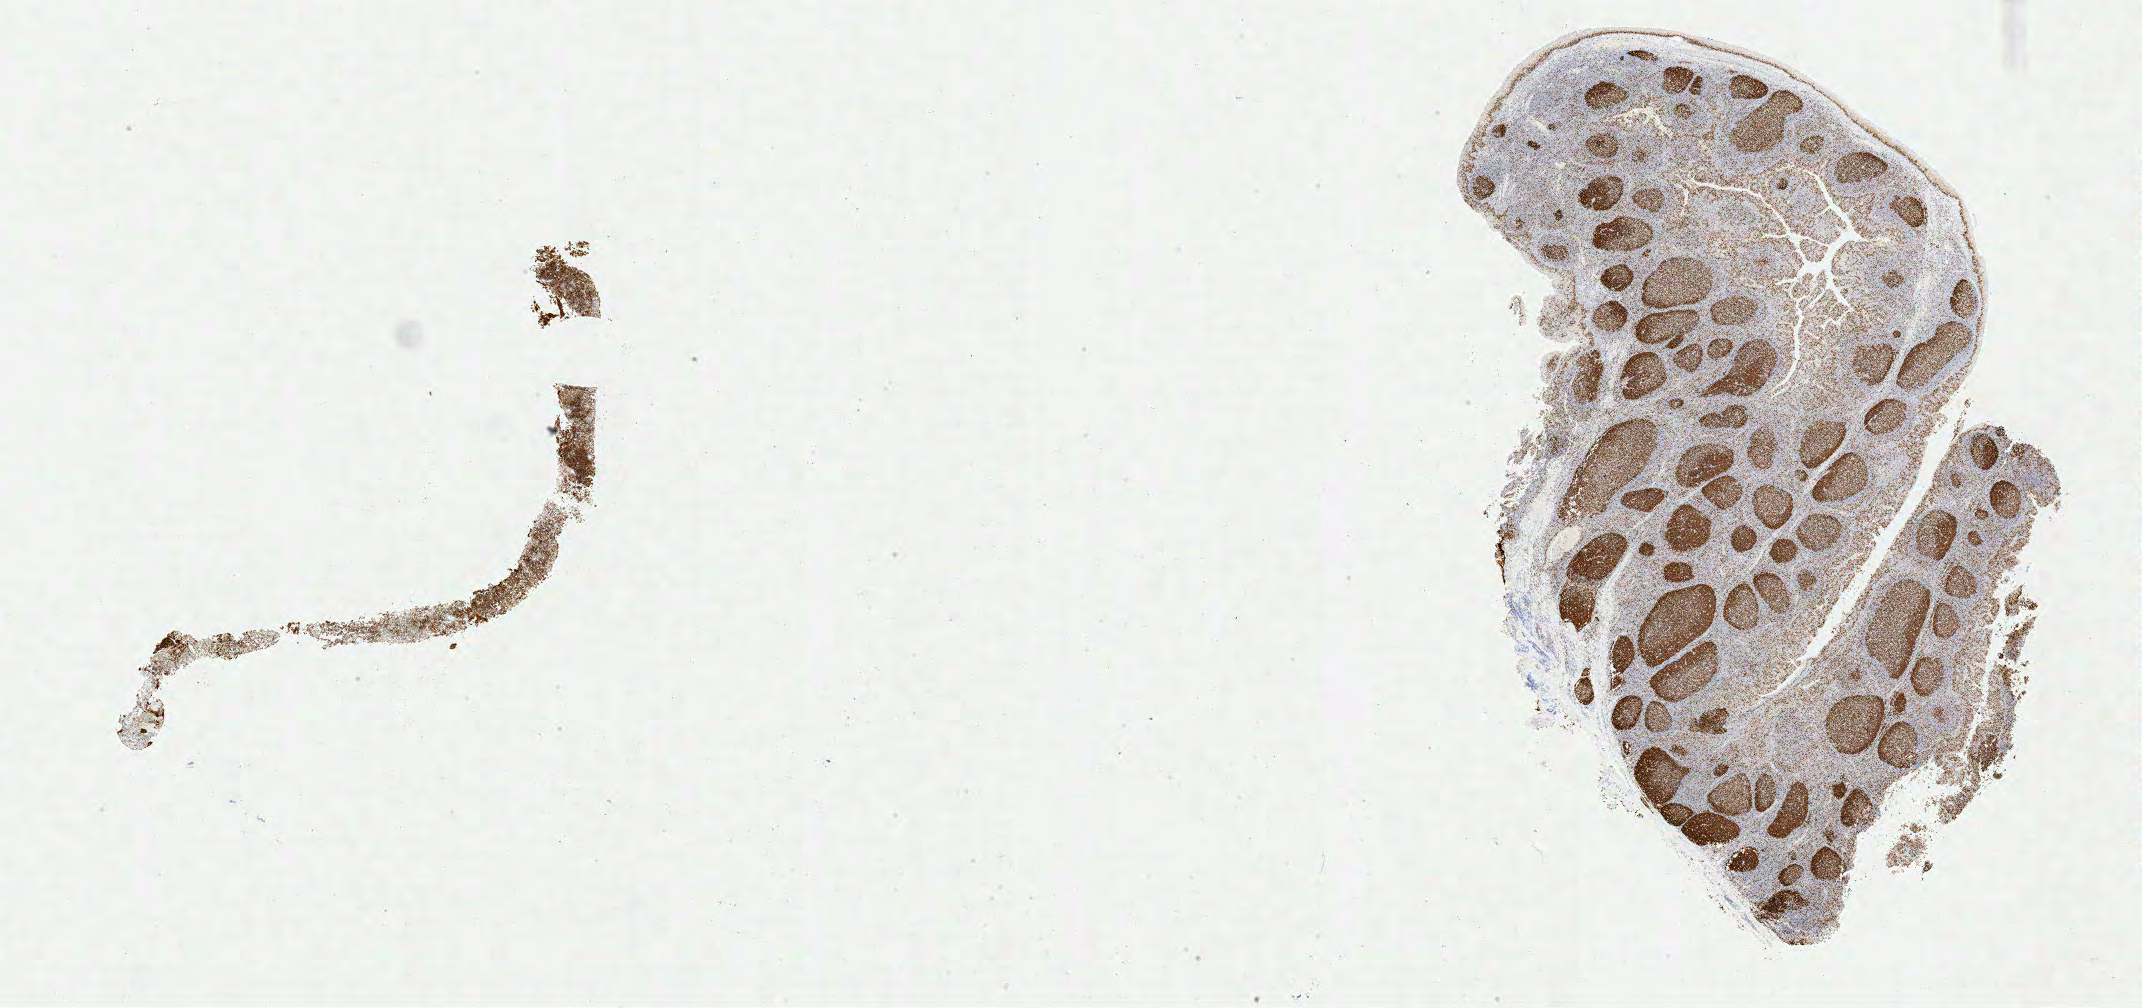
Immunohistochemistry (IHC) whole-slide image stained for Ki-67, low-resolution overview of the scanned area, about 33.8 x 15.9 mm, specimen: tumor tissue, anatomic site: ovary. Patient: female, age at initial diagnosis 7 years.
• diagnosis: Burkitt lymphoma, NOS